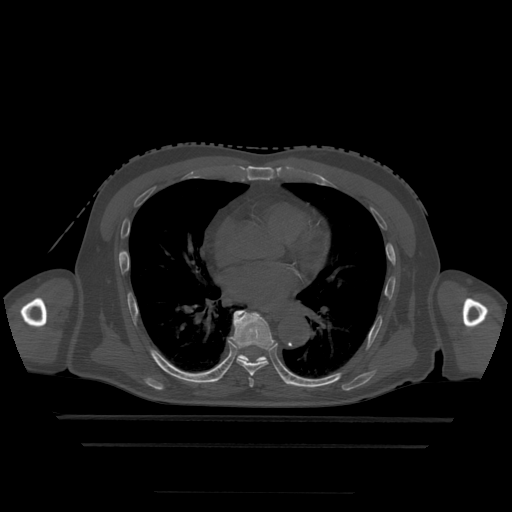
CT including the spine, one axial slice. Slice 294 of 522 in the series (ordered by position). Bone window (W 1800 / L 400 HU). 512 × 512 image matrix, field of view 436 × 436 mm. Patient age 68 years. Case-level facts recorded for this patient, not image findings: primary cancer: urothelial.
Structures marked on this image (semi-automatic segmentation, software-assisted and operator-edited):
- T6 vertebra: box from (x=249, y=378) to (x=254, y=388) px
- T7 vertebra: (x=231, y=311)–(x=274, y=376)
- T8 vertebra: (x=238, y=354)–(x=268, y=363)